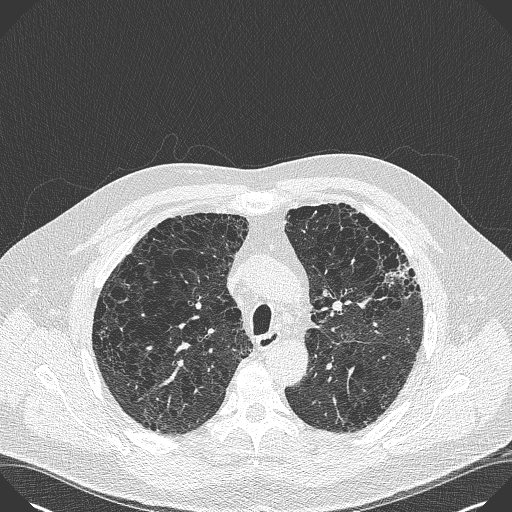
Low-dose screening chest CT, axial slice; baseline annual screen; lung window (W 1500 / L -600 HU); lung (sharp) reconstruction kernel (B50f). Male participant, aged 59 years at enrolment. Current smoker at enrolment.
Expert reader's lesion annotation, box from (x=375, y=241) to (x=428, y=292) px. No non-calcified nodule or mass ≥4 mm was recorded by the screening reader at this exam. Official screen result: negative screen, minor abnormalities not suspicious for lung cancer. Participant outcome: lung cancer diagnosed 909 days after this screen (after the third annual screen) — bronchiolo-alveolar carcinoma, mixed mucinous and non-mucinous, left upper lobe, stage IA (AJCC 6th edition), 20 mm at pathology.